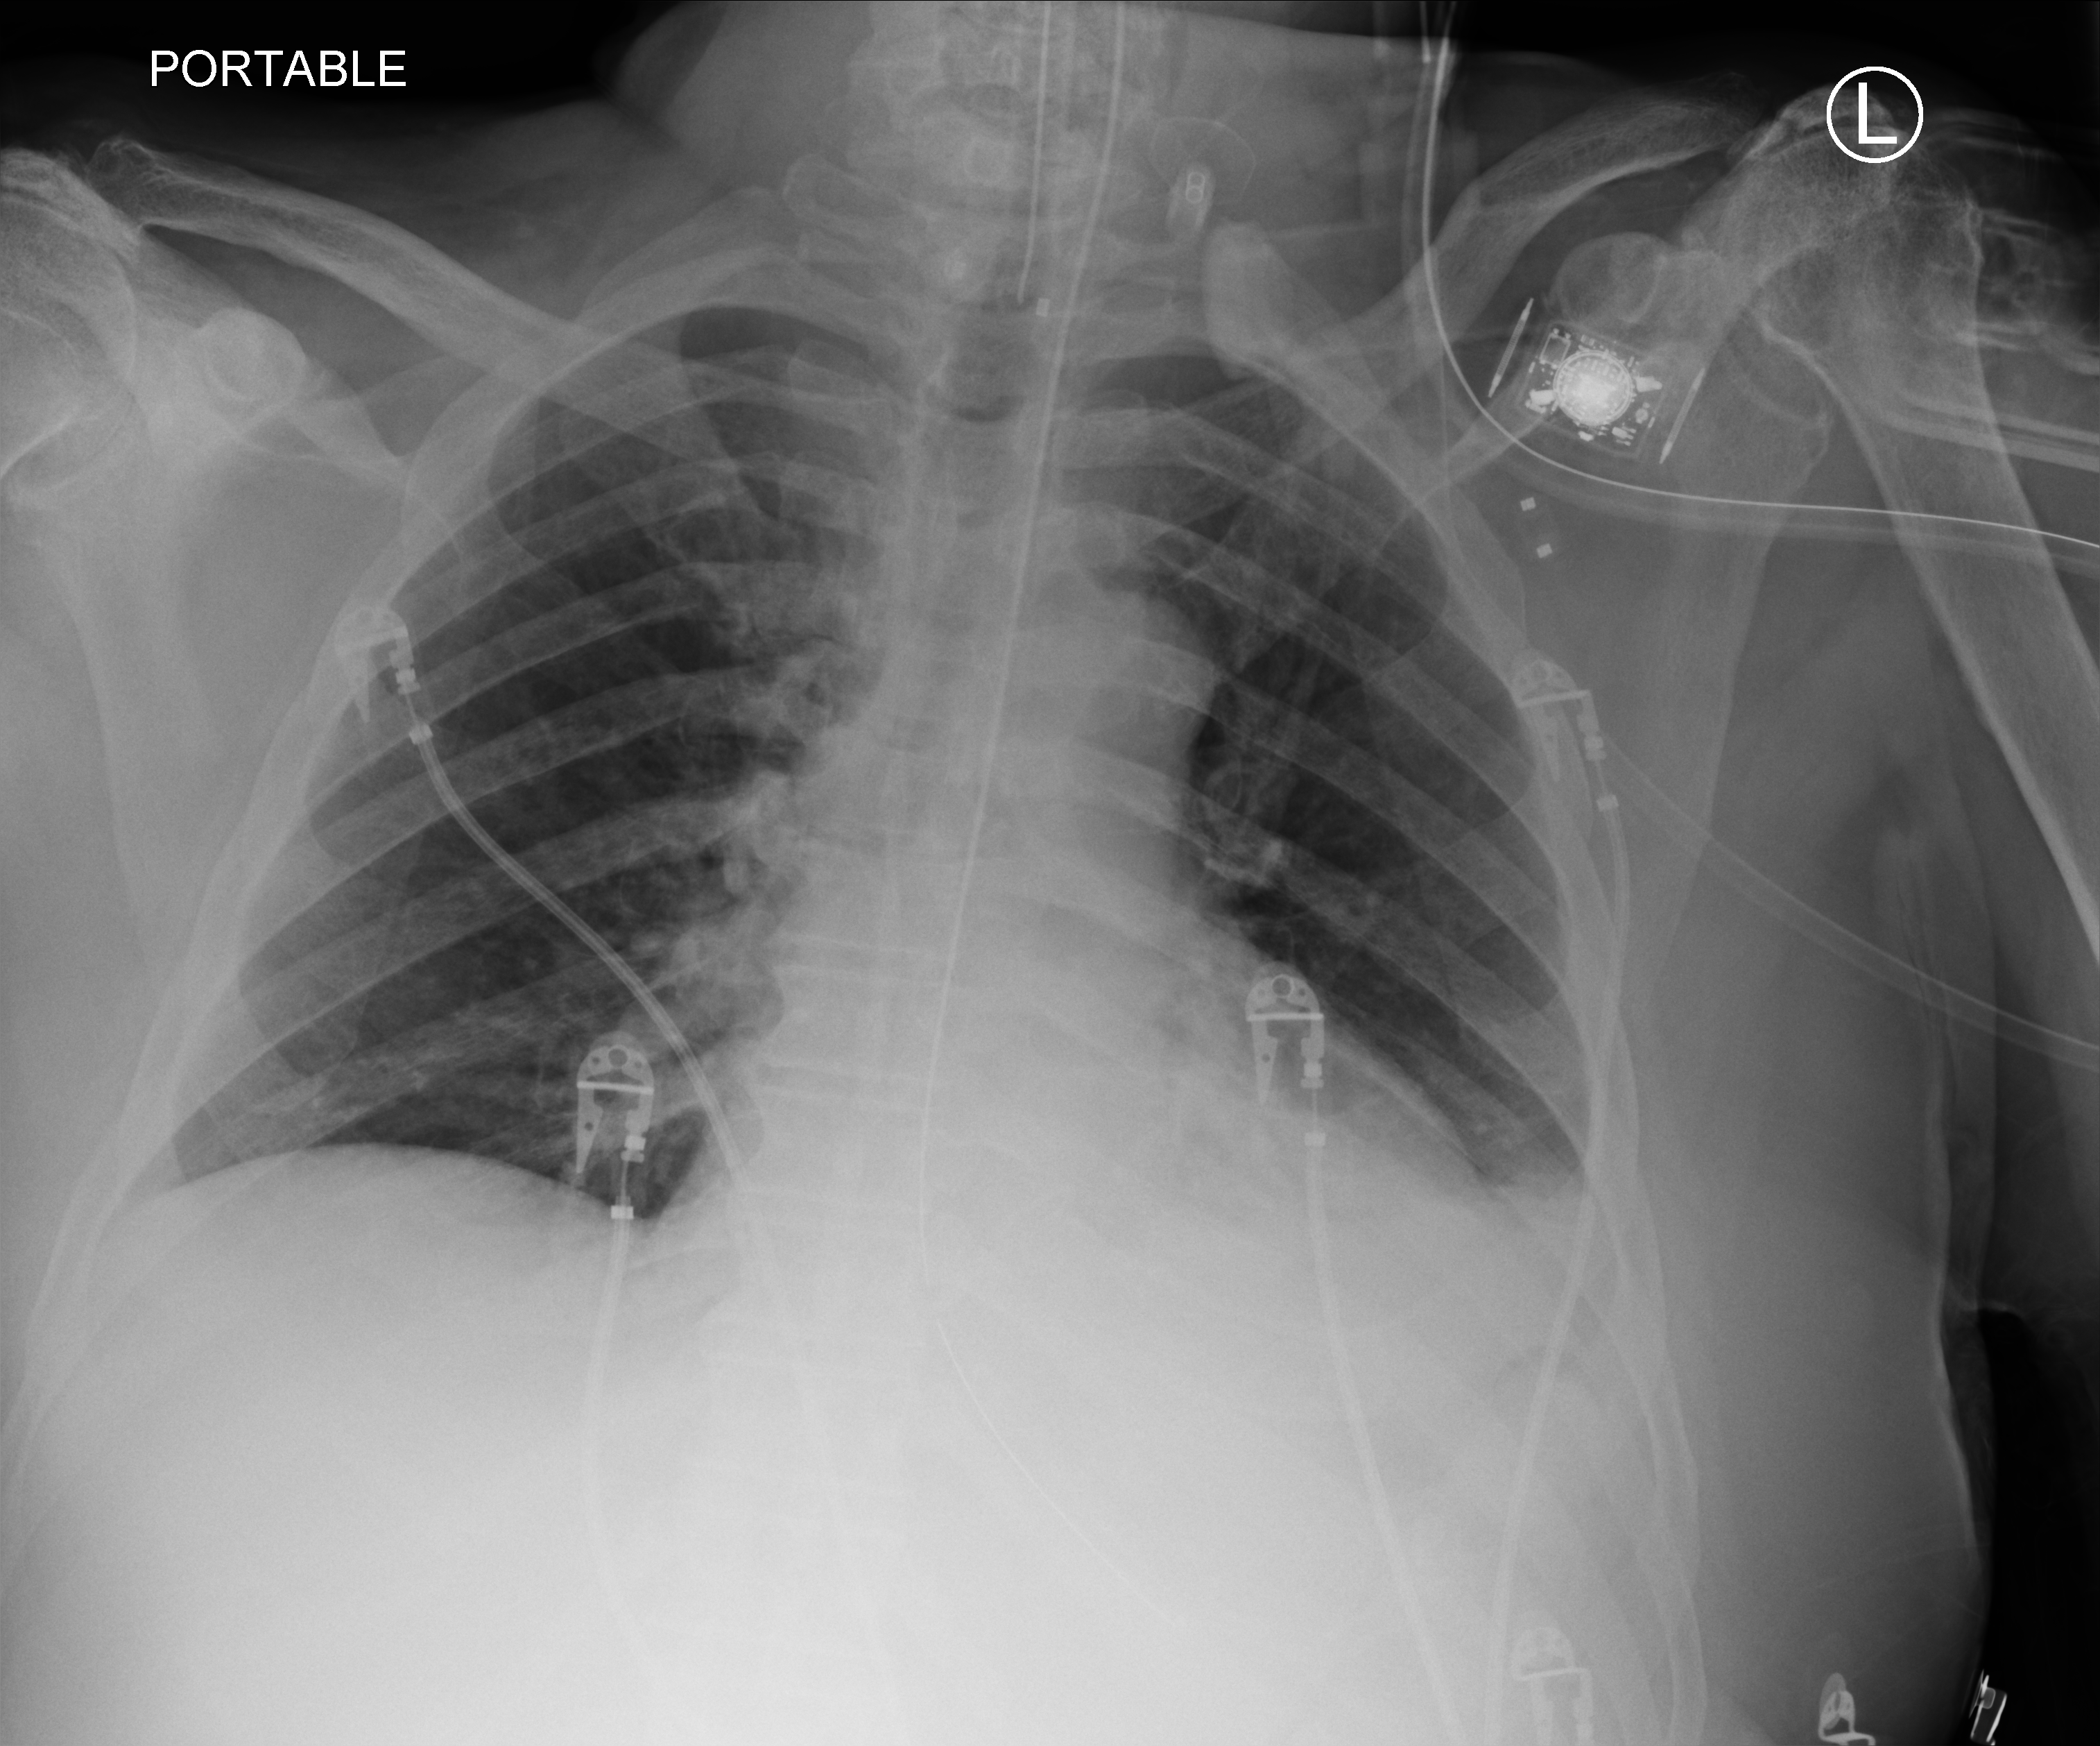
Chest X-ray (portable), anteroposterior (AP) projection. Patient hospitalised with COVID-19; male, aged 75–90 years.
From the hospital-stay record, not from the radiograph (when in the stay this image was taken is not recorded):
- smoking status (admission record): former
- mechanically ventilated during this hospital stay: yes